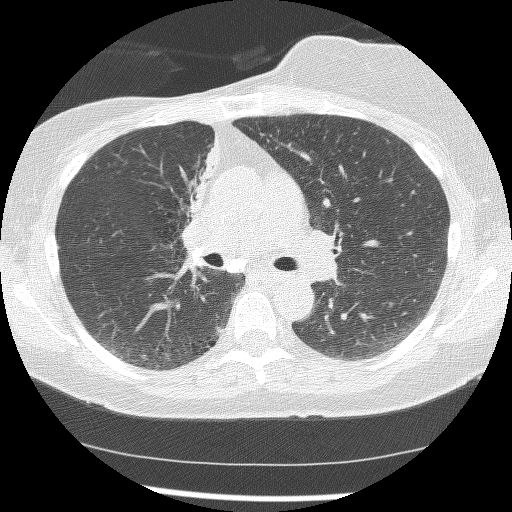
Chest CT (low-dose screening protocol), one axial image; baseline annual screen; lung window (W 1500 / L -600 HU); 512 × 512 image matrix. Female, age 56 years at enrolment. Current smoker at enrolment.
Expert reader's lesion annotation, bounding box [x1, y1, x2, y2] px = [161, 141, 216, 256]. The screening reader recorded 2 non-calcified nodules or masses ≥4 mm on this exam (right lower lobe, right middle lobe); which of them this box marks is not recorded.